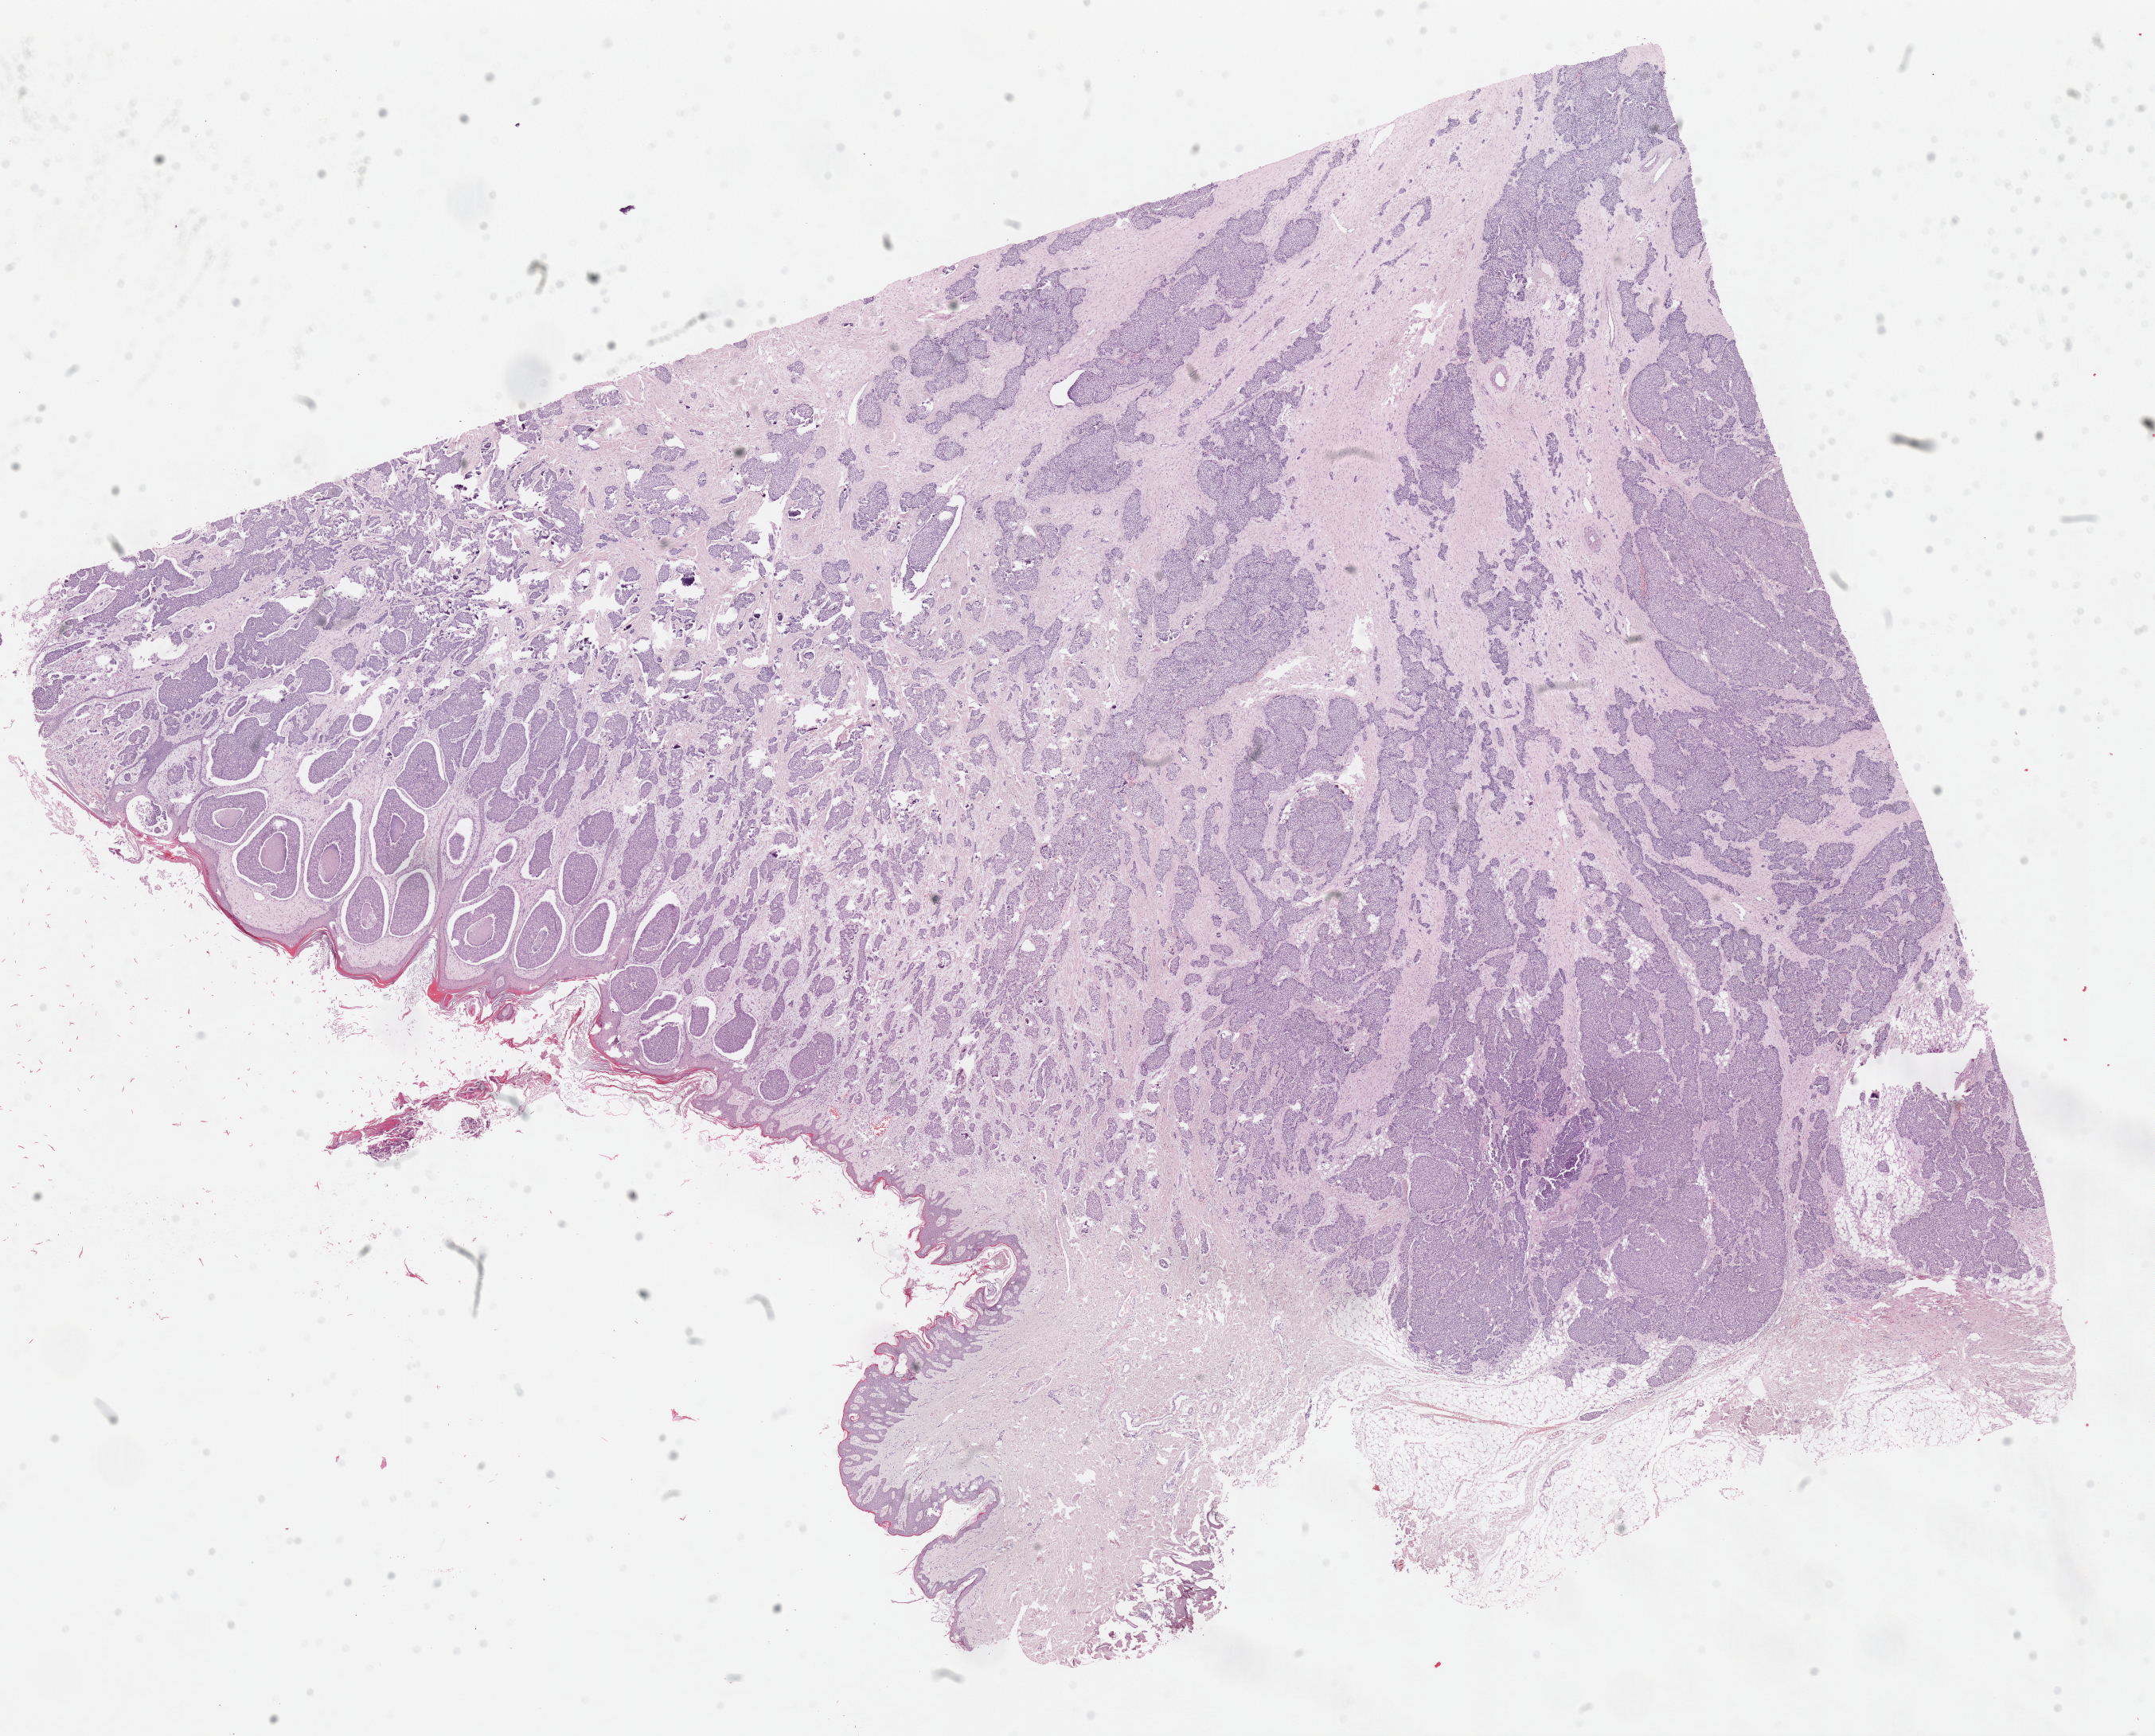
Whole-slide histology image, H&E, shown as a low-resolution overview of the whole scanned area (about 21.4 x 17.2 mm, acquisition: 40x scan). Formalin-fixed paraffin-embedded (FFPE) diagnostic section. Primary tumour sample from the breast. Patient: female, age at initial diagnosis 86 years.
* AJCC pathologic stage: IIIB (7th edition)
* TNM: T4b N1a M0
* laterality: right
* histologic diagnosis: Infiltrating duct carcinoma, NOS